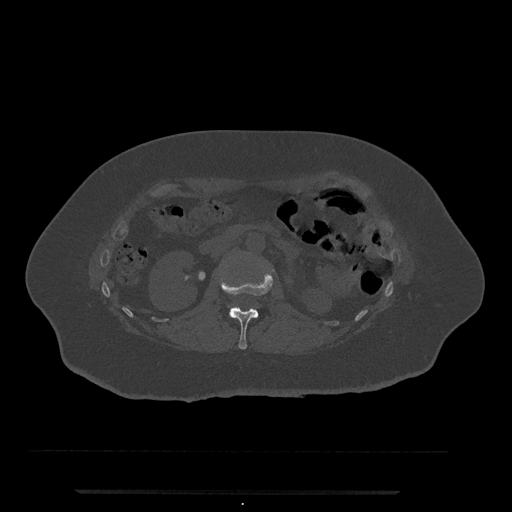
CT including the spine, one axial slice; reconstruction kernel Br40s/3; bone window (W 1800 / L 400 HU); 0.5 mm slice thickness; 512 × 512 image matrix, field of view 440 × 440 mm. Patient: female, 51 years. From the clinical record (not read from this slice): primary cancer: neuro.
Annotated regions visible in this slice (semi-automatic segmentation, software-assisted and operator-edited):
- L1 vertebra: bounding box <219,269,274,350> (left, top, right, bottom; pixels)
- L2 vertebra: <229,306,239,311>